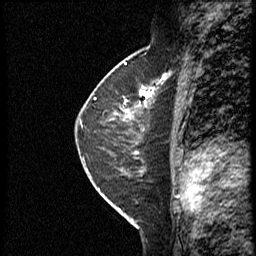
Breast MRI (dynamic contrast-enhanced), one sagittal slice. Position 22 of 40 along the scan axis. Dynamic contrast-enhanced study with each time point stored as its own series, time point 2 of 4 at this slice position (early post-contrast, ordered by acquisition time). 1.5 T. TE 4.2 ms, TR 18.8 ms. 256 × 256 image matrix, field of view 200 × 200 mm. Female patient. Case-level facts recorded for this patient, not image findings: setting: breast cancer imaged before/during neoadjuvant chemotherapy; receptor status: HER2-positive.
Structures marked on this image (semi-automatic segmentation, software-assisted and operator-edited):
- analysis volume of interest (the breast-tissue region the enhancement analysis was run in; not a lesion): bounding box [x1, y1, x2, y2] px = [91, 79, 169, 153]
- tumour enhancement mask (voxels above the 100 % enhancement threshold inside the analysis volume of interest): [95, 87, 156, 118]